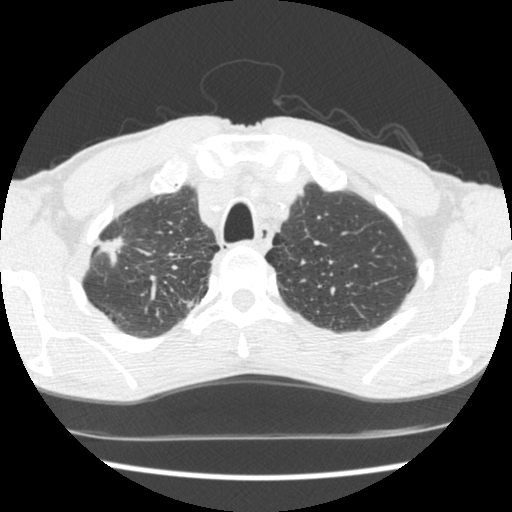
Low-dose screening chest CT, axial slice. First (baseline) screen. Lung window (W 1500 / L -600 HU). Standard (soft-tissue) reconstruction kernel (STANDARD). 120 kVp. Slice 37 of 197 in the series. 512 × 512 image matrix. Male participant, aged 62 years at enrolment. Current smoker at enrolment.
• Expert reader's lesion annotation, box from (x=83, y=221) to (x=136, y=274) px.
• Screening reader's record for this exam: no non-calcified nodule ≥4 mm recorded.
• Later outcome: lung cancer diagnosed 640 days after this screen (after the second annual screen) — adenocarcinoma, NOS, right upper lobe, poorly differentiated (G3), stage IIA (AJCC 6th edition), 22 mm at pathology.